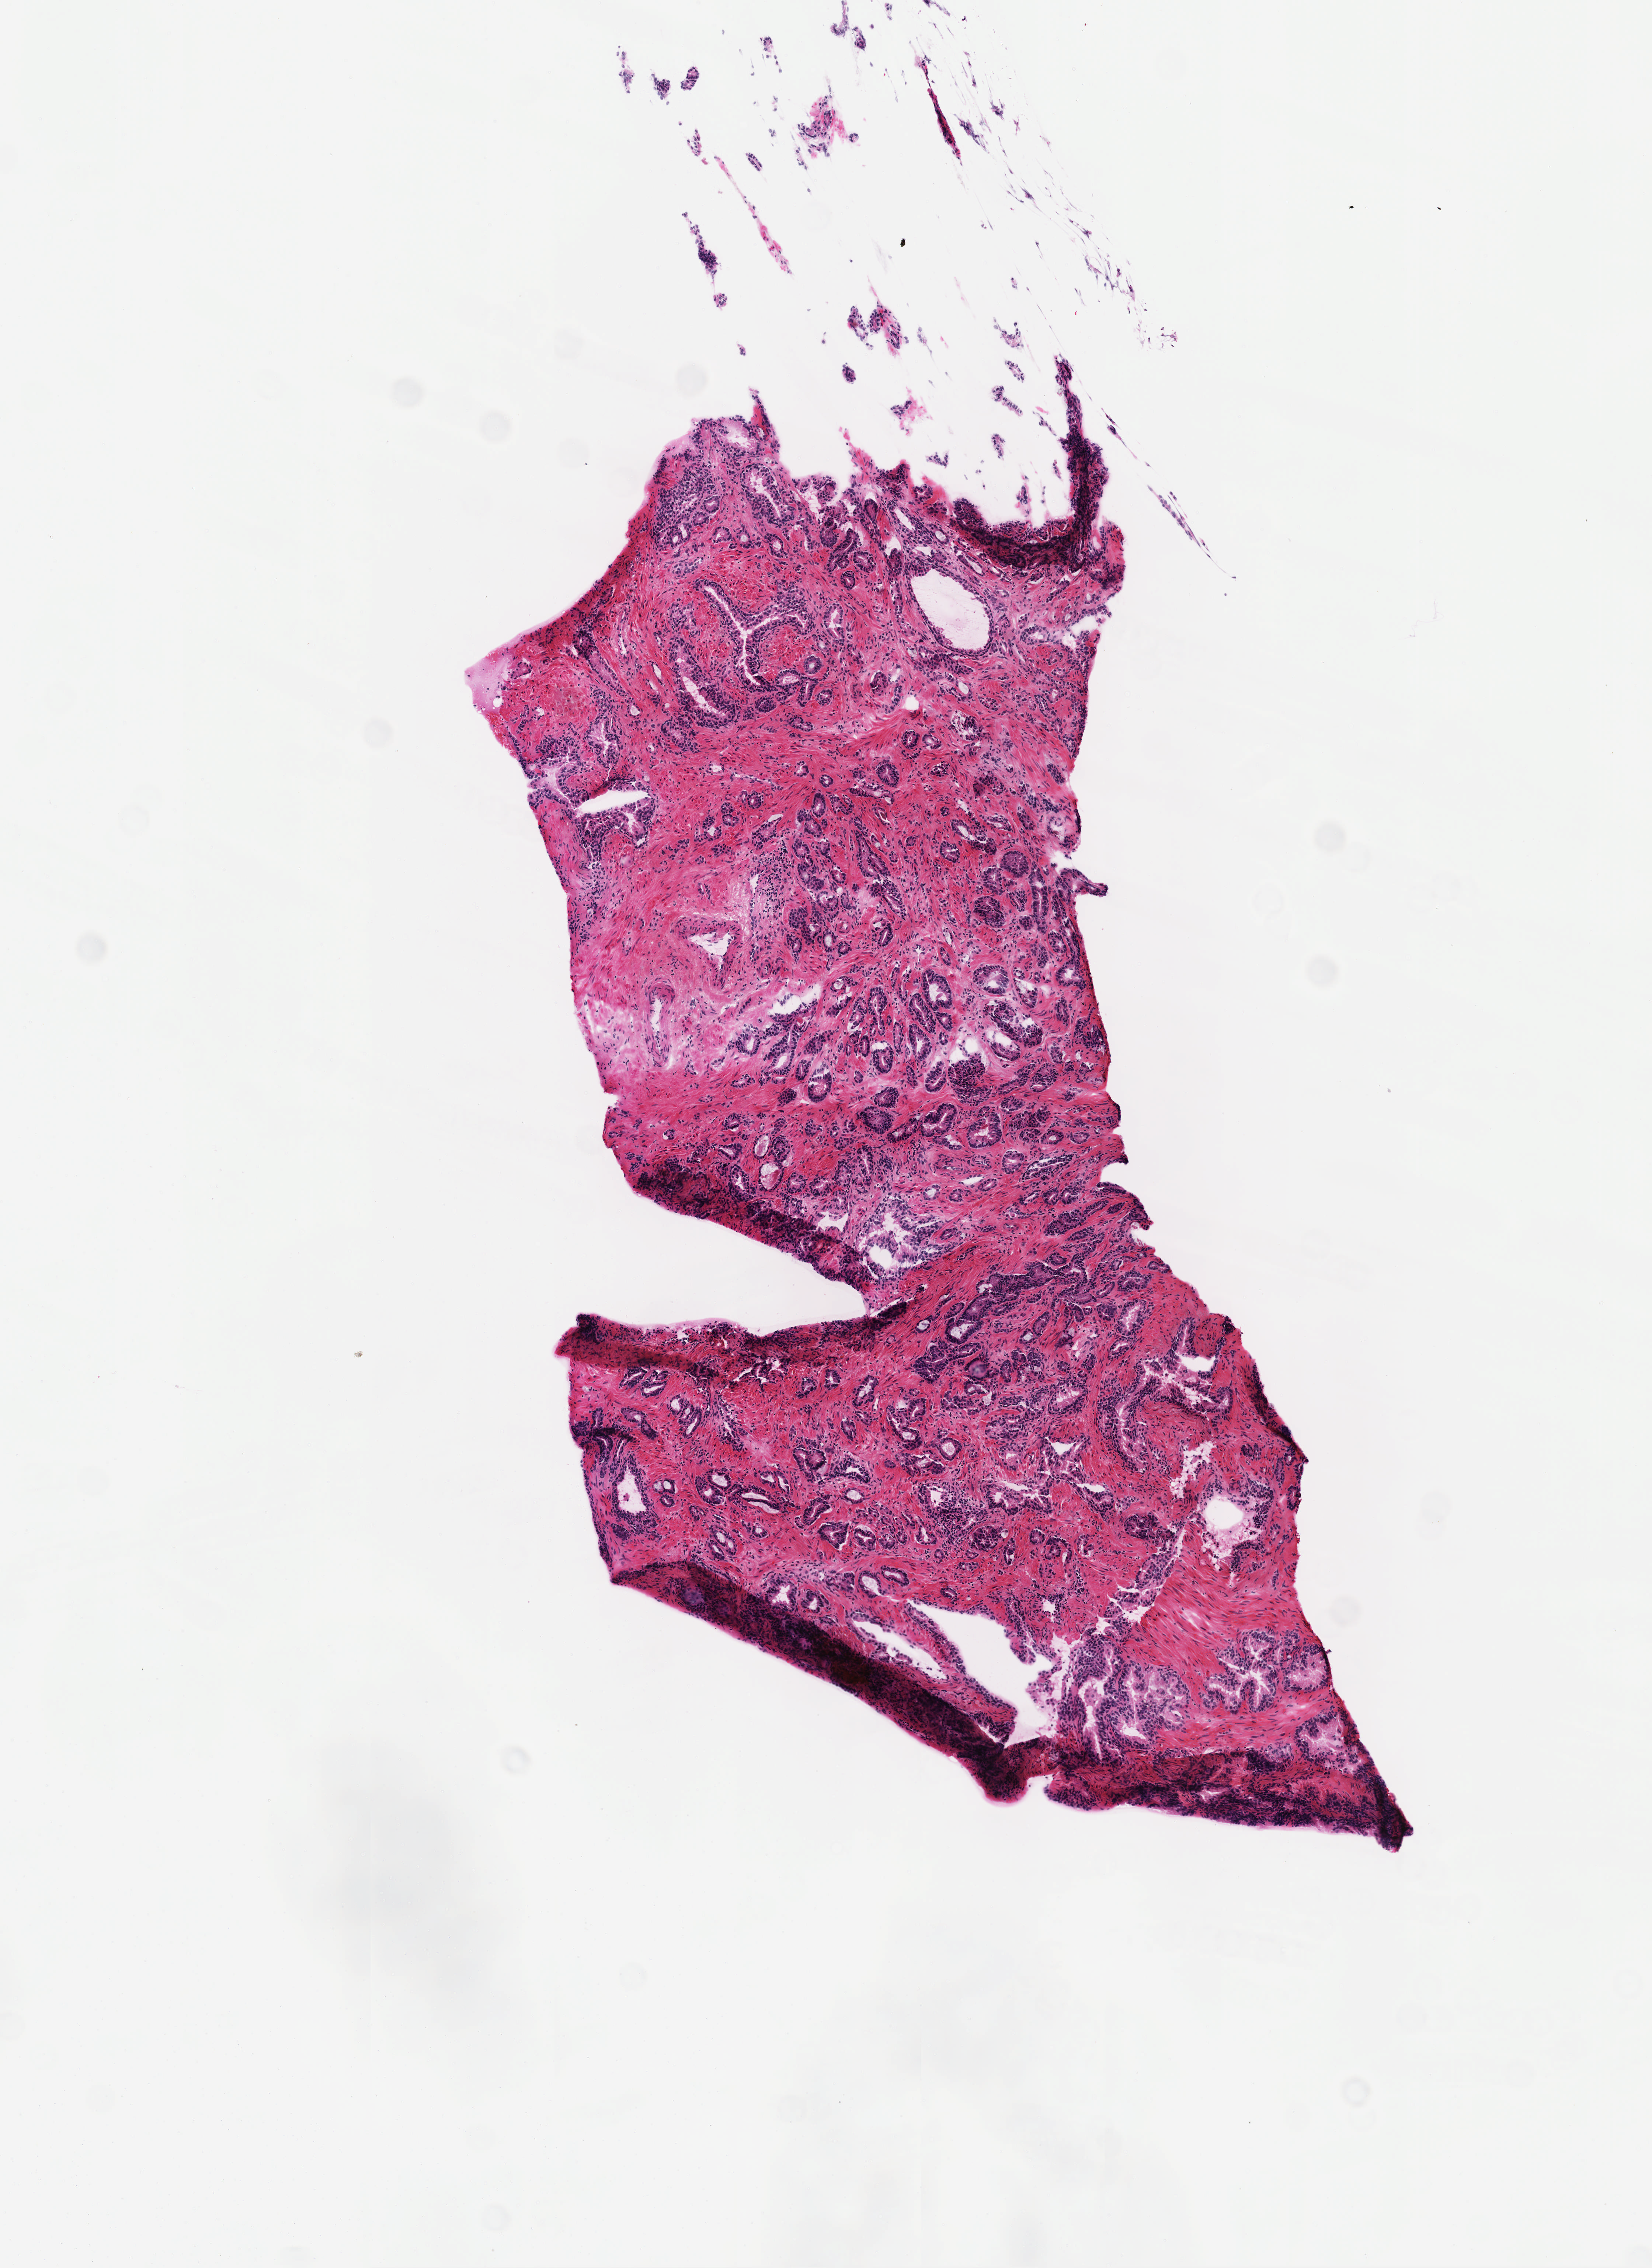
H&E whole-slide image, shown as a low-resolution overview of the whole scanned area (about 4.5 x 6.2 mm, acquisition: 40x scan); frozen section; primary tumour sample from the prostate. Patient: male, age at initial diagnosis 48 years. Gleason score: 6 (3+3). Composition of this section per pathologist review: tumour cells 30%, tumour nuclei 75%, normal cells 18%, stromal cells 52%, necrosis 0%. Infiltration values recorded for this section: lymphocyte infiltration 4%, monocyte infiltration 0%, neutrophil infiltration 0%.
Diagnosis: Adenocarcinoma, NOS (prostate gland). Laterality: right.